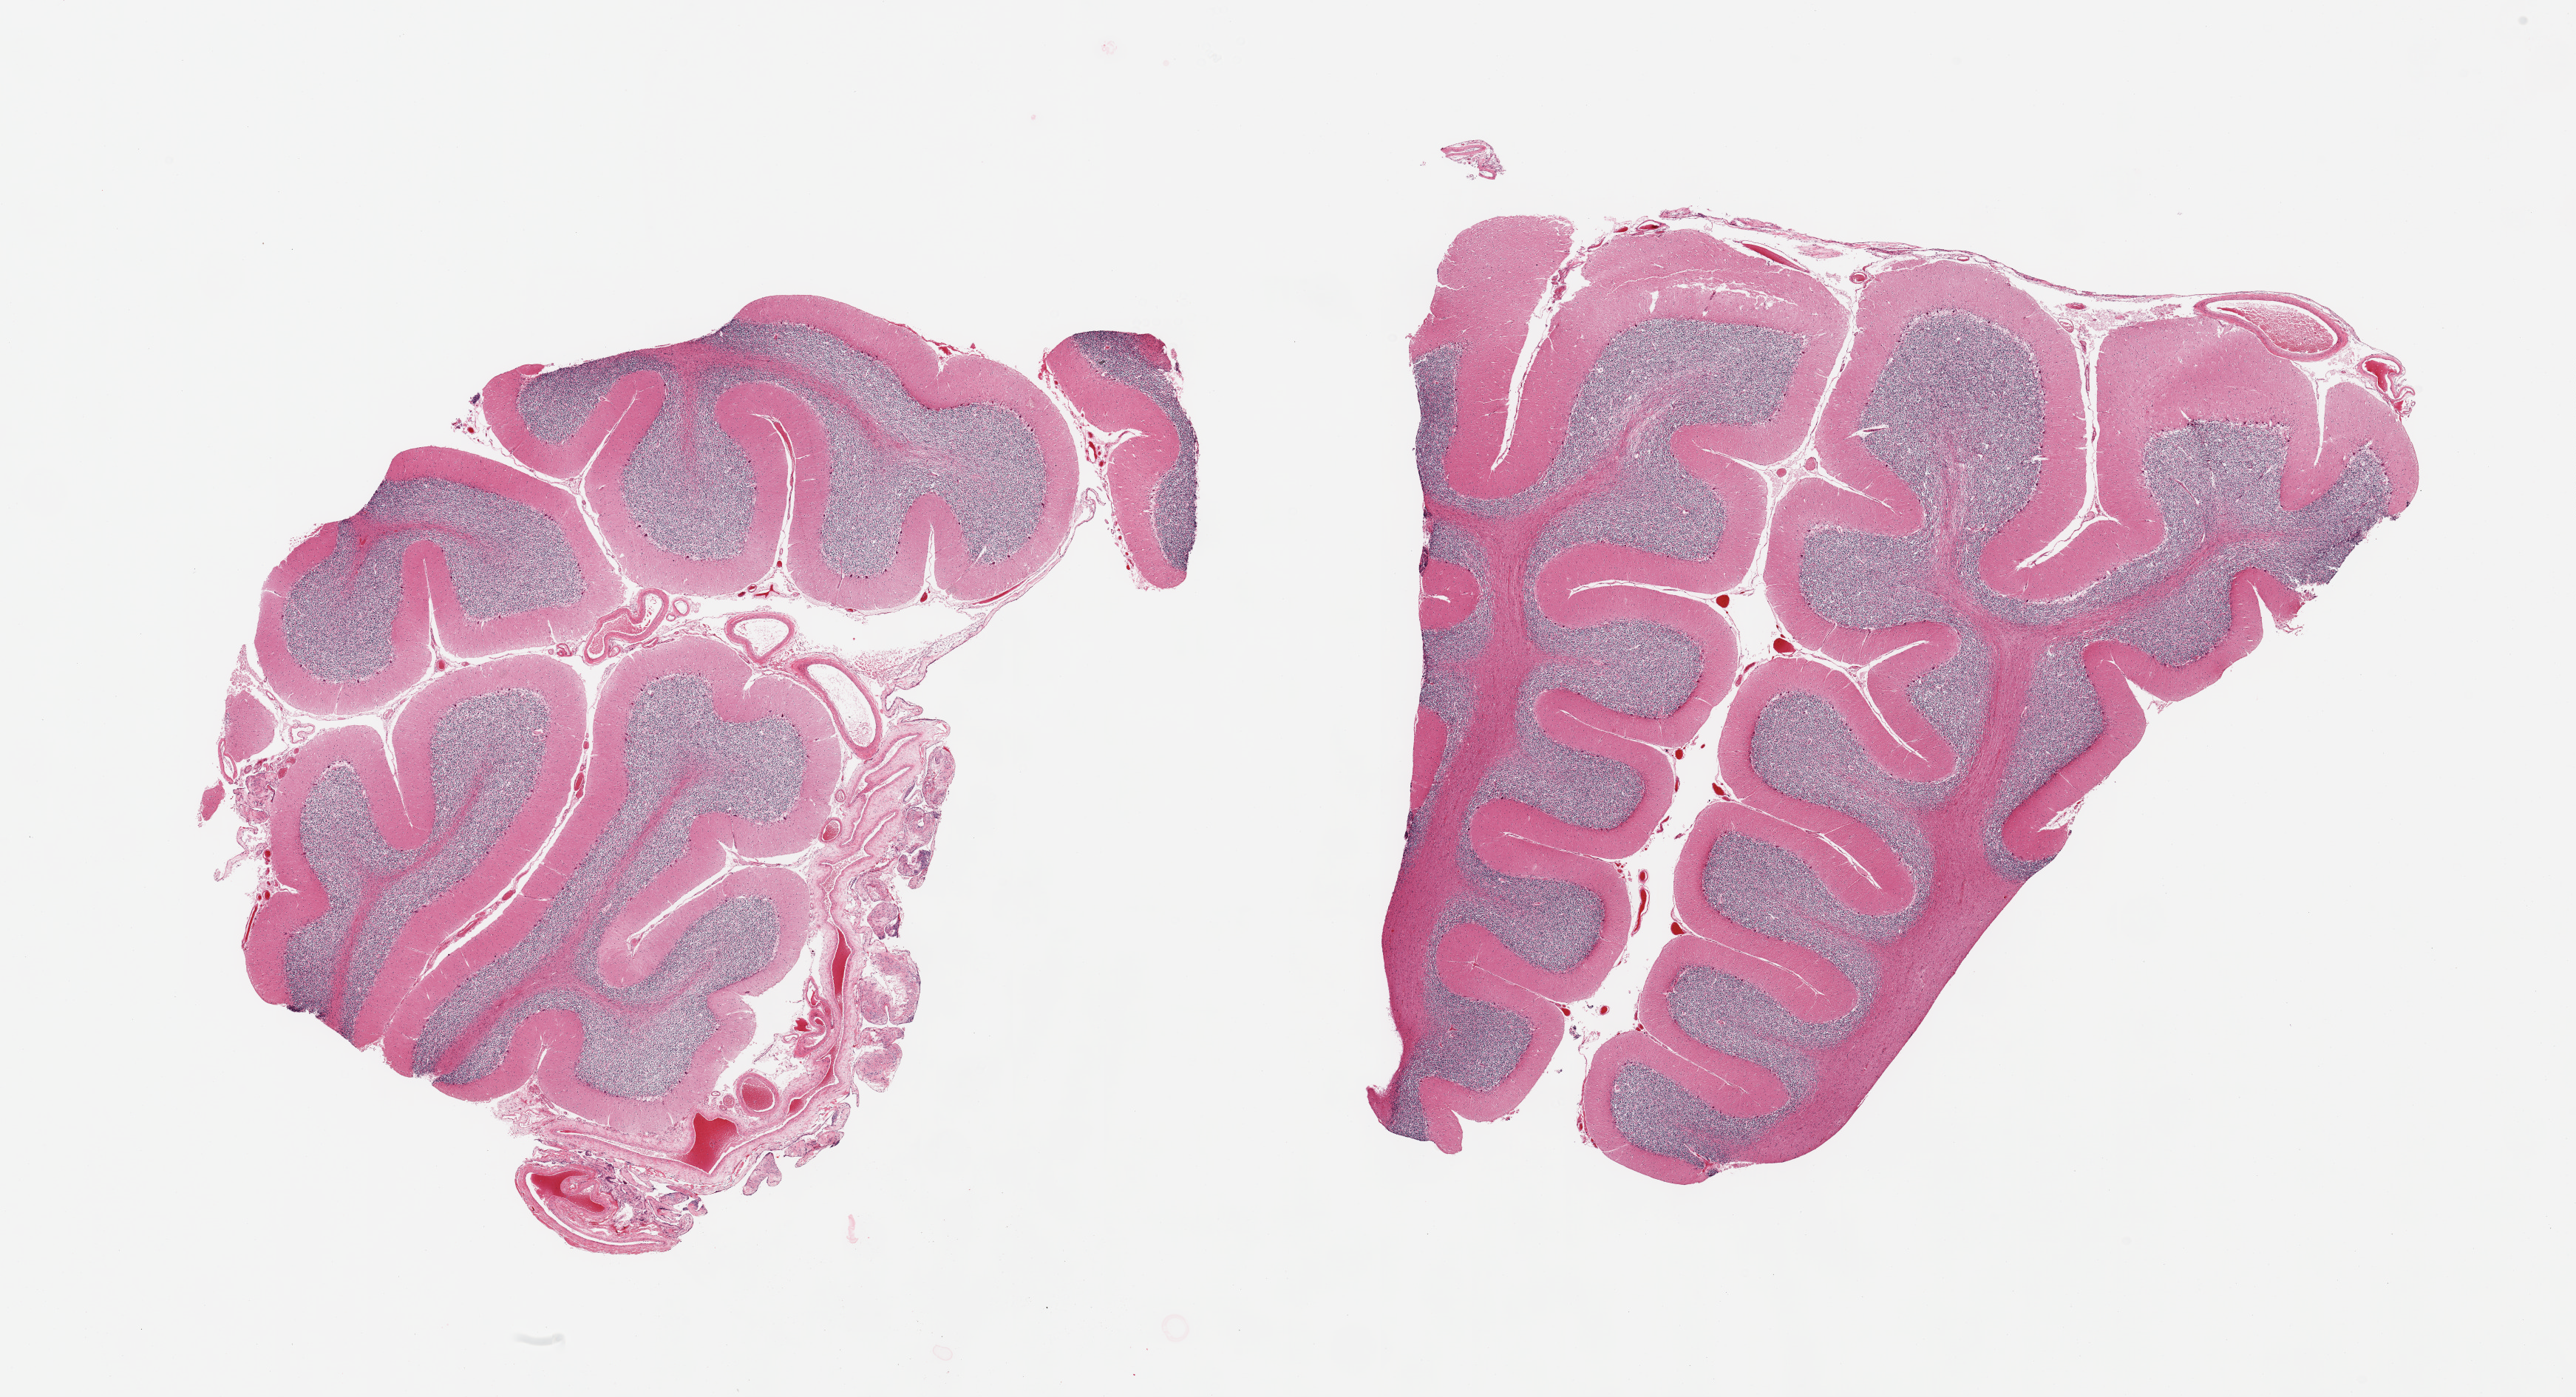
Digitized hematoxylin and eosin (H&E)-stained section — low-resolution overview of the scanned area, about 27.6 x 14.9 mm (acquisition: 20x scan); PAXgene-fixed paraffin-embedded (PFPE) section; section of cerebellum (target tissue); donor tissue sample.
* reviewer comment on this tissue sample: 2 pieces; cerebellum with thick layer of meninges